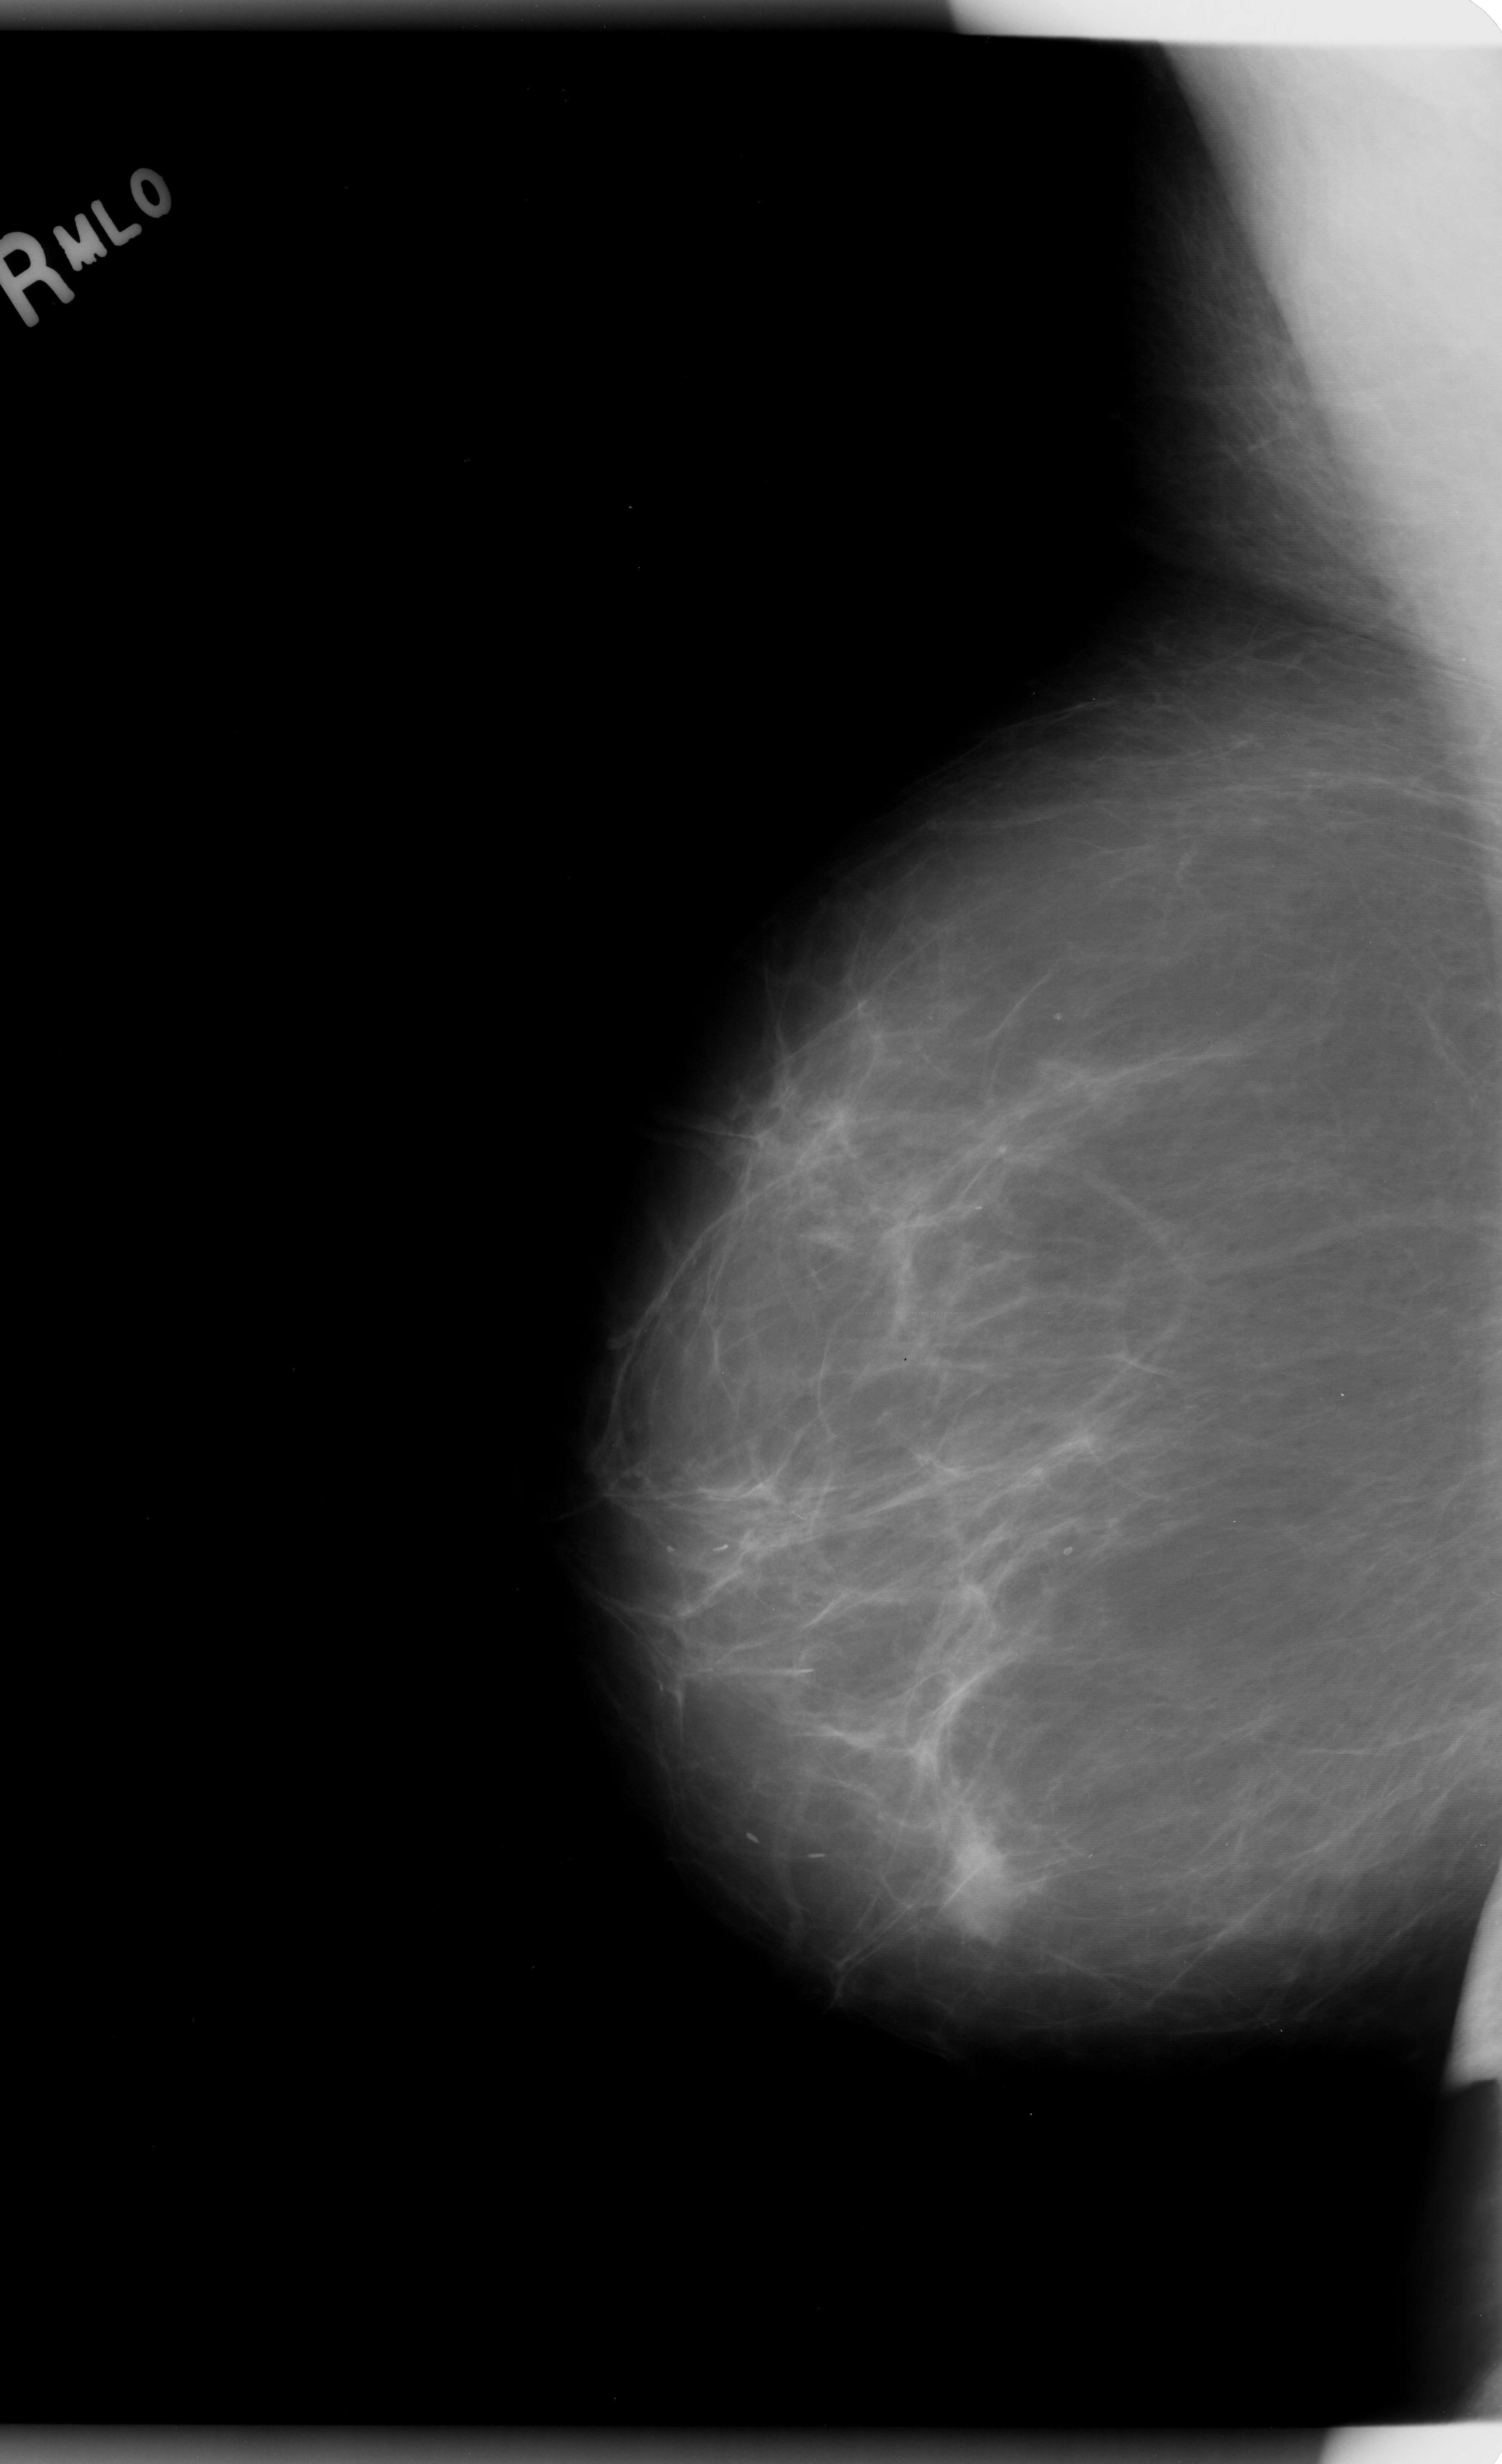
Scanned film-screen mammogram. Right breast. Mediolateral oblique (MLO) view. Breast composition: almost entirely fatty (BI-RADS density category 1 of 4). 1502 × 2464 image matrix.
Expert-marked regions of interest on this image (one box per marked abnormality):
- mass, shape oval, margins microlobulated; BI-RADS assessment category 5; pathology (as recorded): malignant: bounding box [x1, y1, x2, y2] px = [916, 1801, 1039, 1949]